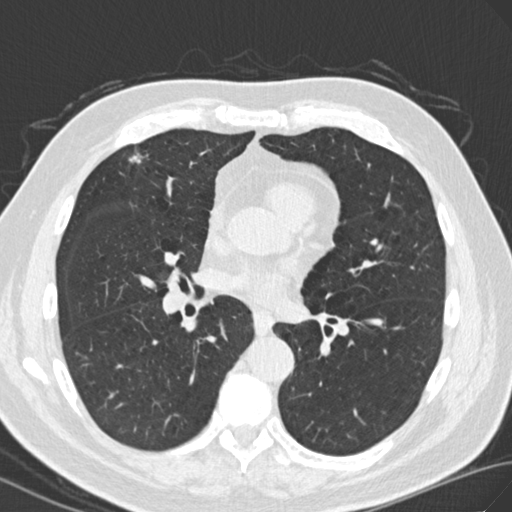
Chest CT (low-dose screening protocol), one axial image; second annual screen; lung window (W 1500 / L -600 HU); standard (soft-tissue) reconstruction kernel (B30f); slice 90 of 171 in the series; 512 × 512 image matrix. Male, age 69 years at enrolment. Current smoker at enrolment.
Expert reader's lesion annotation, bounding box (x1, y1, x2, y2) in pixels: (111, 139, 160, 181). The screening reader recorded 3 non-calcified nodules or masses ≥4 mm on this exam; which of them this box marks is not recorded. Participant outcome: lung cancer diagnosed 183 days after this screen — adenocarcinoma, NOS, right upper lobe, moderately differentiated (G2), stage IIA (AJCC 6th edition), 20 mm at pathology.